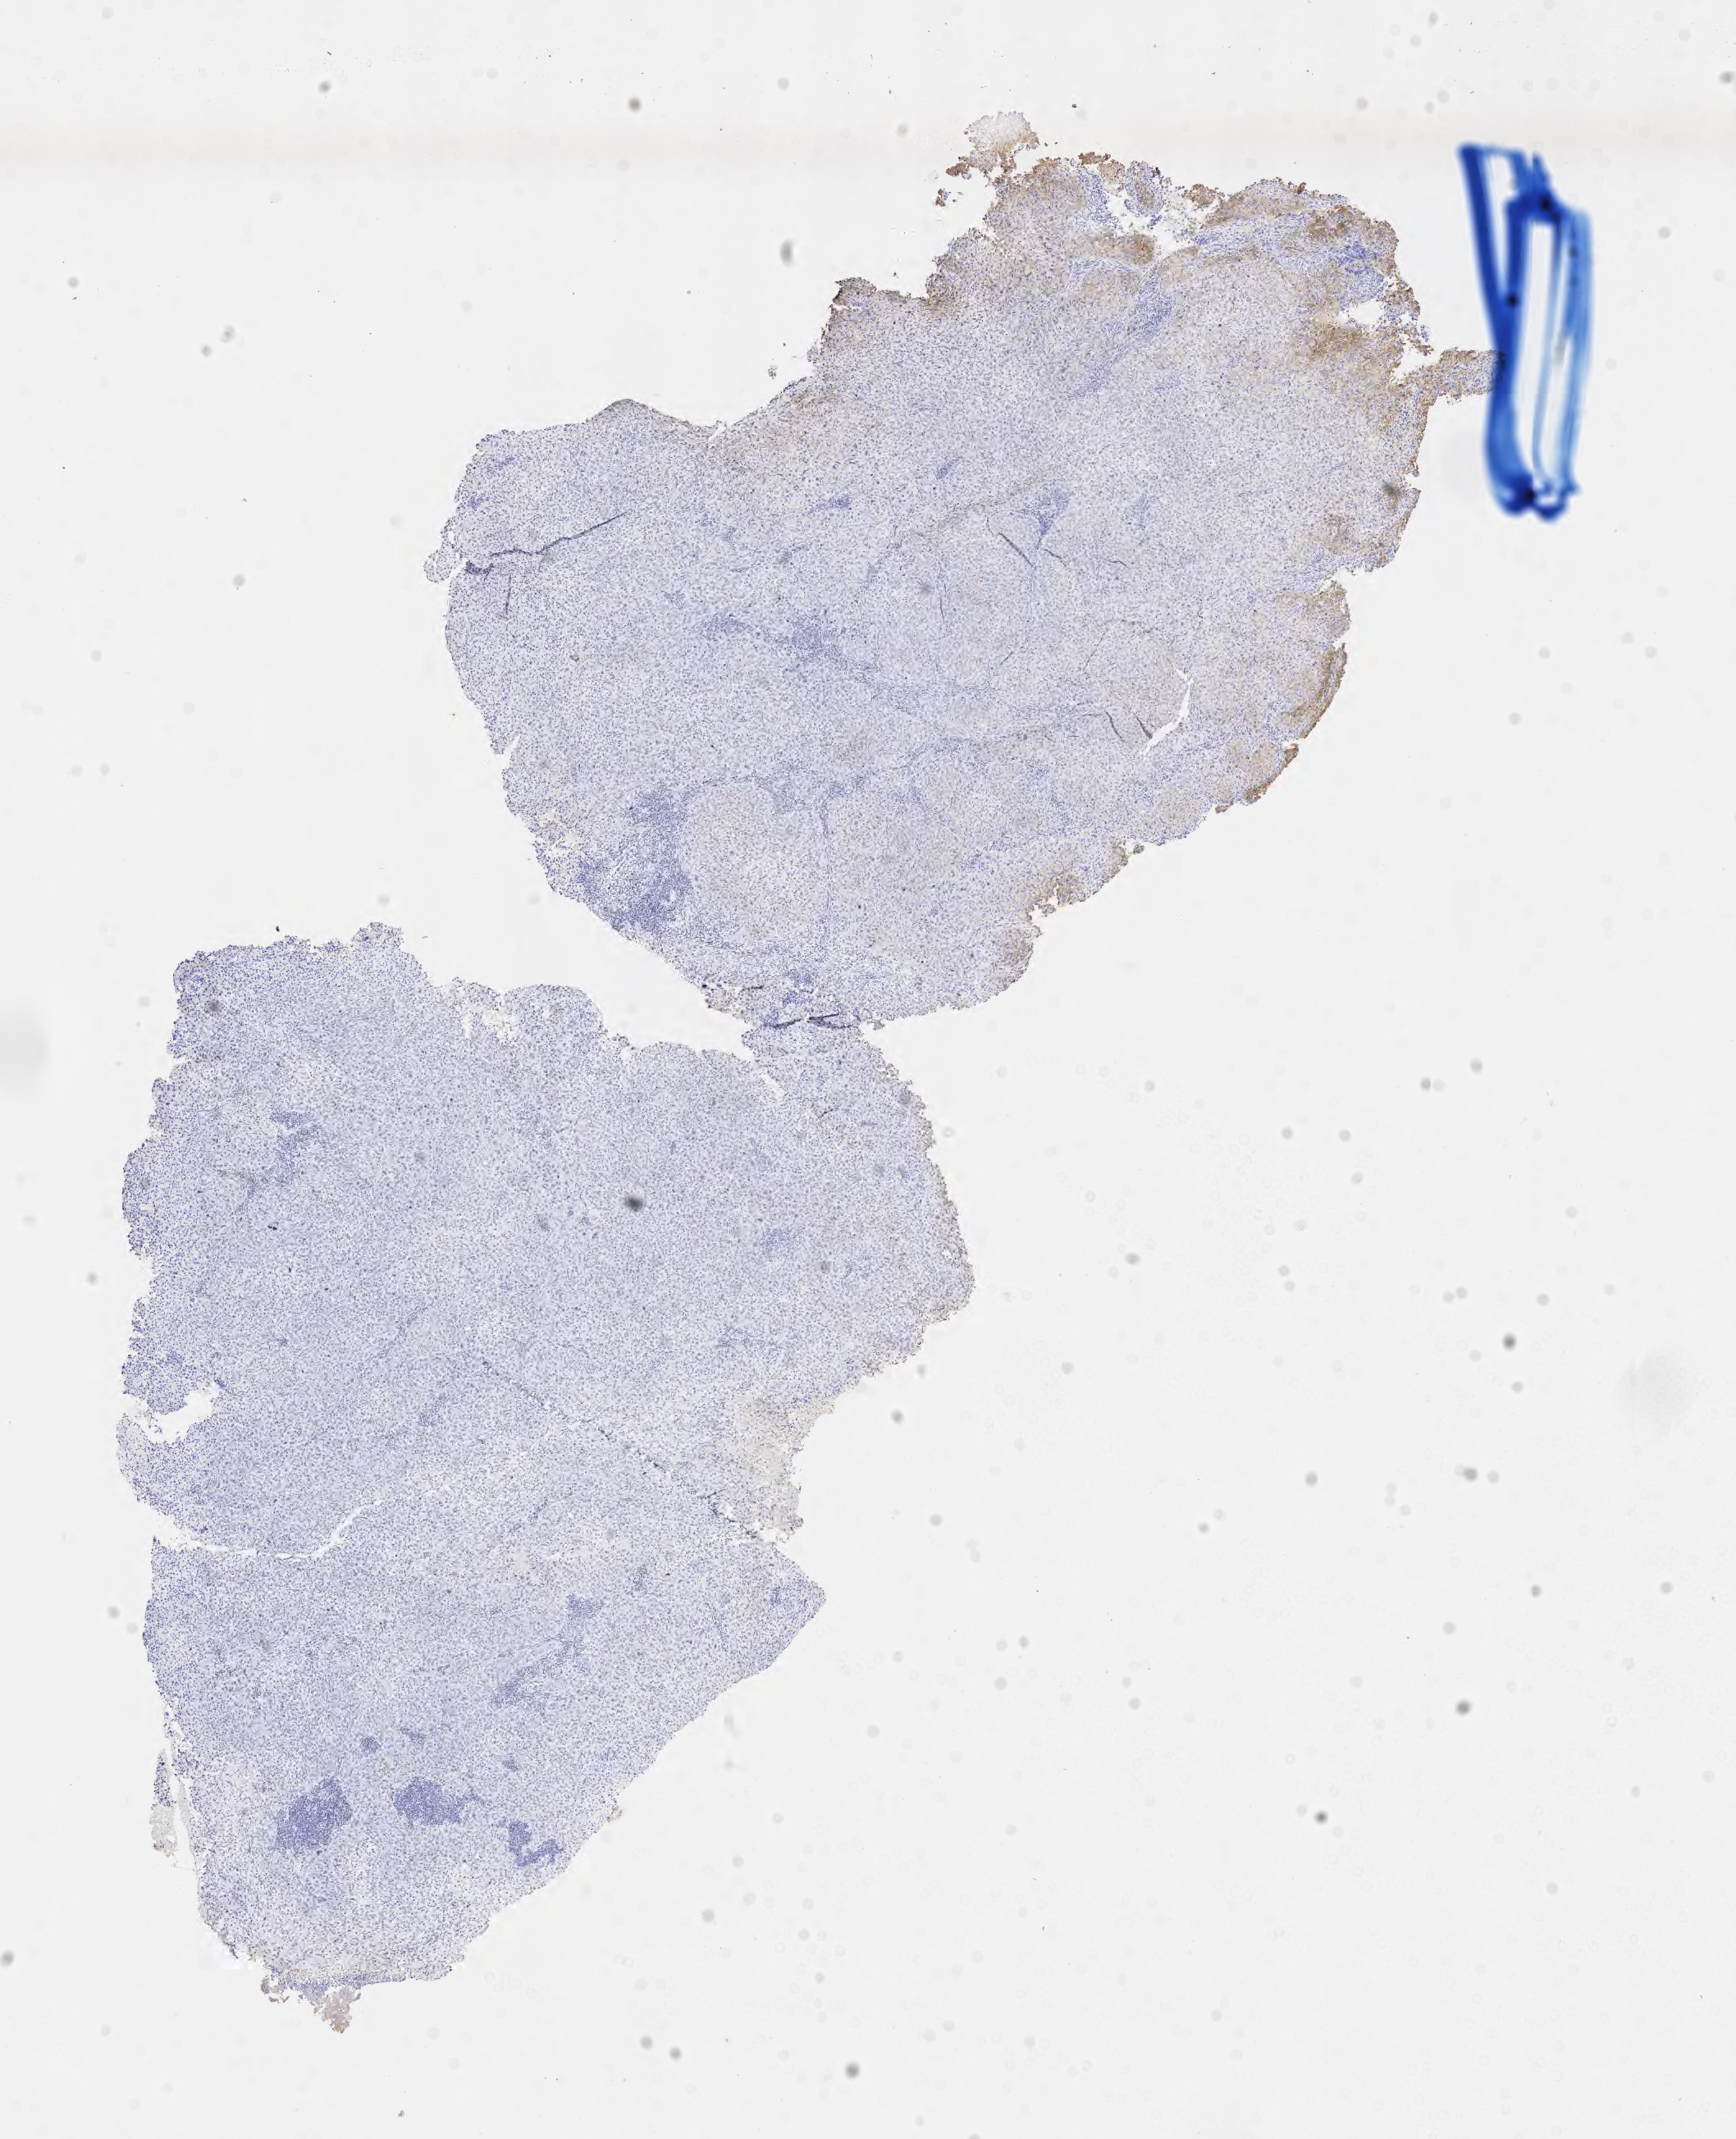
Immunohistochemistry (IHC) whole-slide image stained for MOC-31 (anti-EpCAM), low-resolution overview of the scanned area, about 8.6 x 10.5 mm. Specimen: tumor tissue. Anatomic site: cervix. Patient female; aged 45.
• diagnosis: Squamous cell carcinoma, large cell, nonkeratinizing, NOS